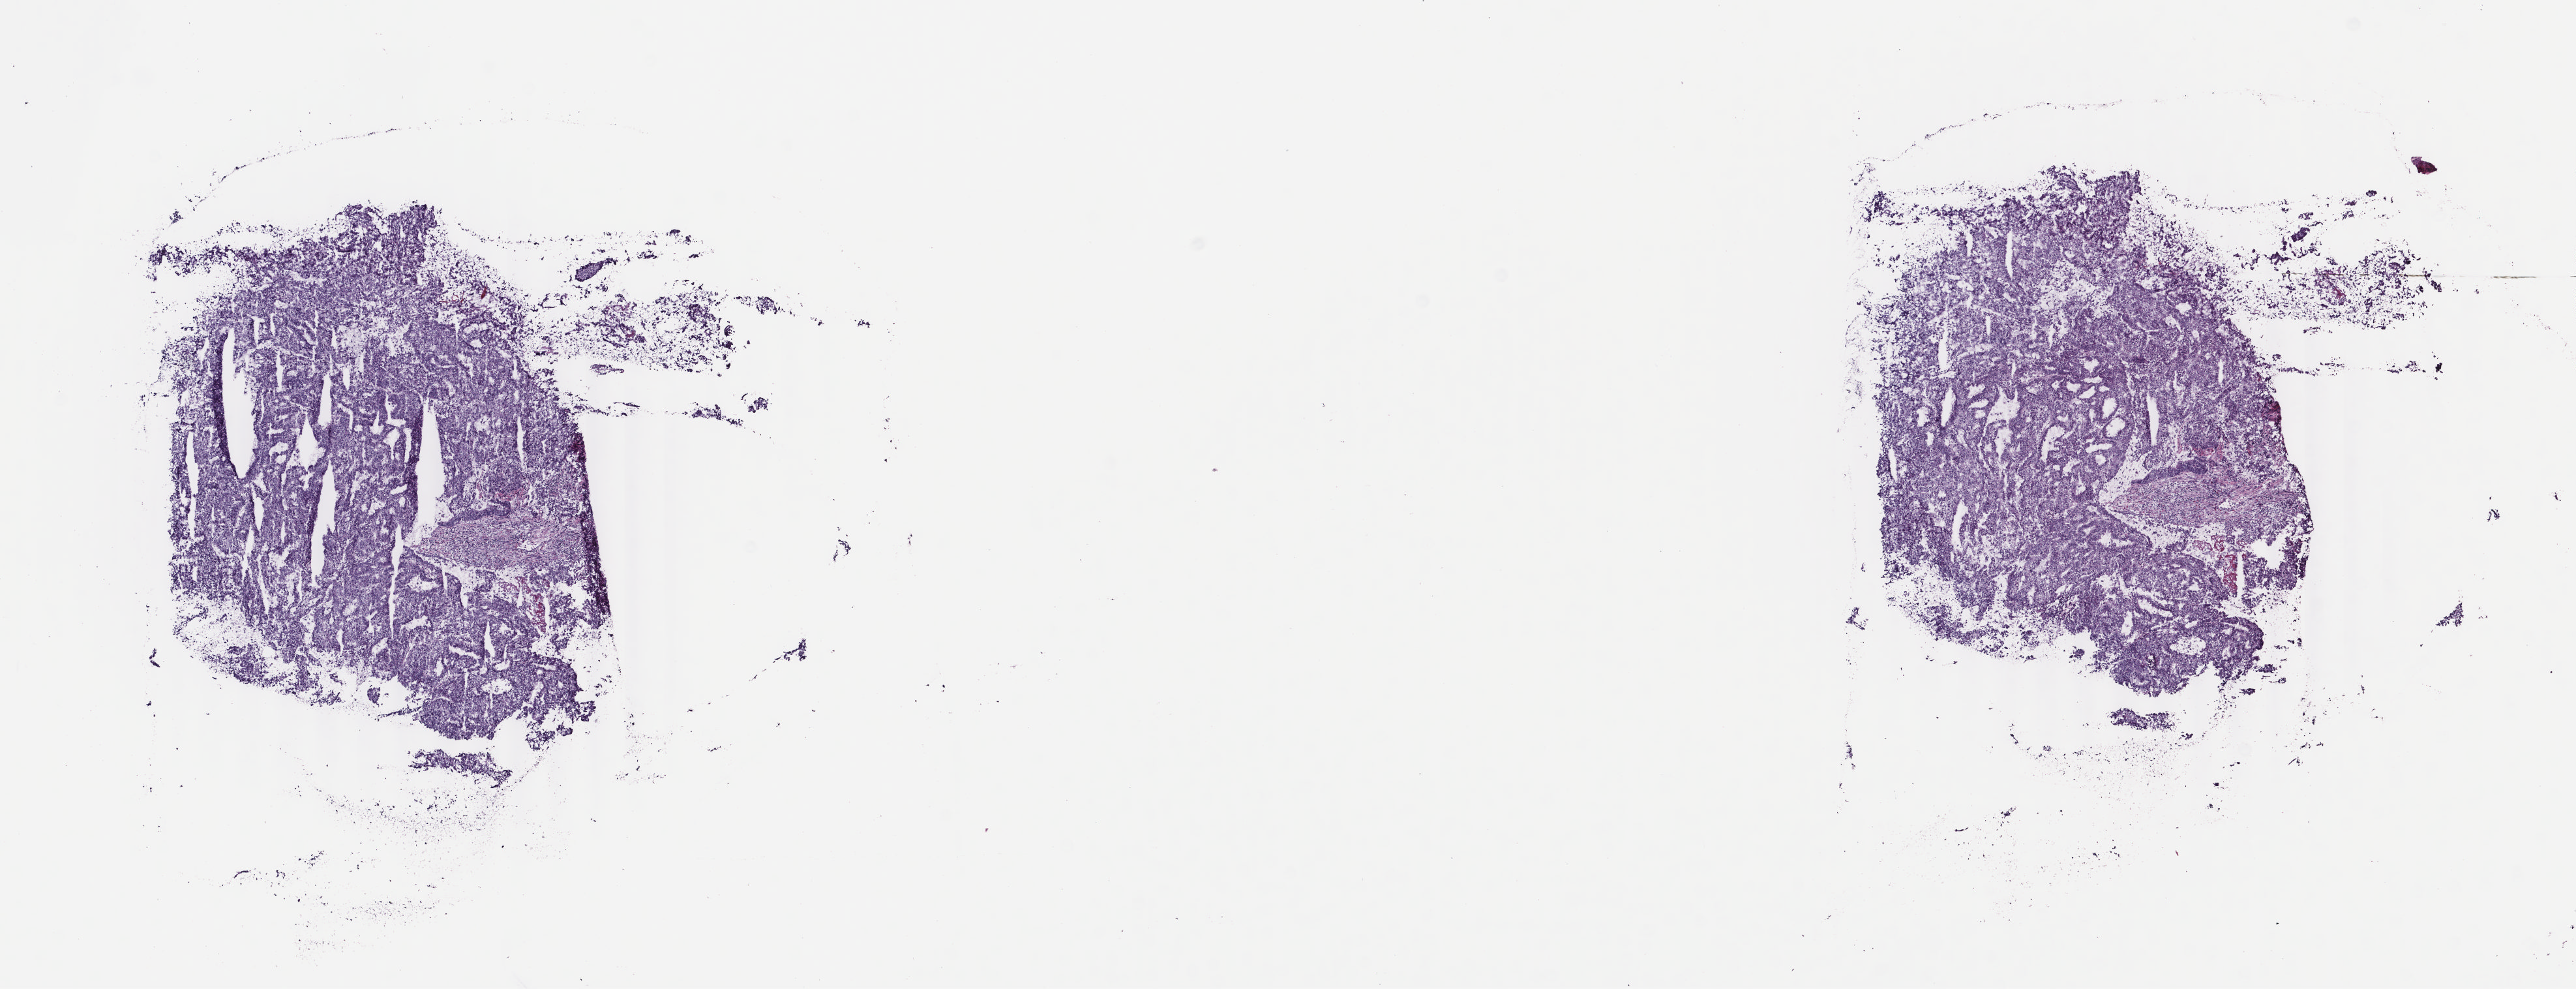
H&E-stained whole-slide image — low-resolution overview of the scanned area, about 15.7 x 6.0 mm (from a 40x scan), frozen section from the top of the tissue portion, sample: primary tumour, uterus. Patient: female, age at initial diagnosis 47 years. Histologic grade: G2 (moderately differentiated). Pathologist review of this section (percent, as recorded): tumour cells 60%, tumour nuclei 80%, normal cells 10%, stromal cells 10%, necrosis 20%. Infiltration values recorded for this section: lymphocyte infiltration 20%, monocyte infiltration 10%, neutrophil infiltration 20%.
* histologic diagnosis: Endometrioid adenocarcinoma, NOS (endometrium)
* FIGO stage: IB